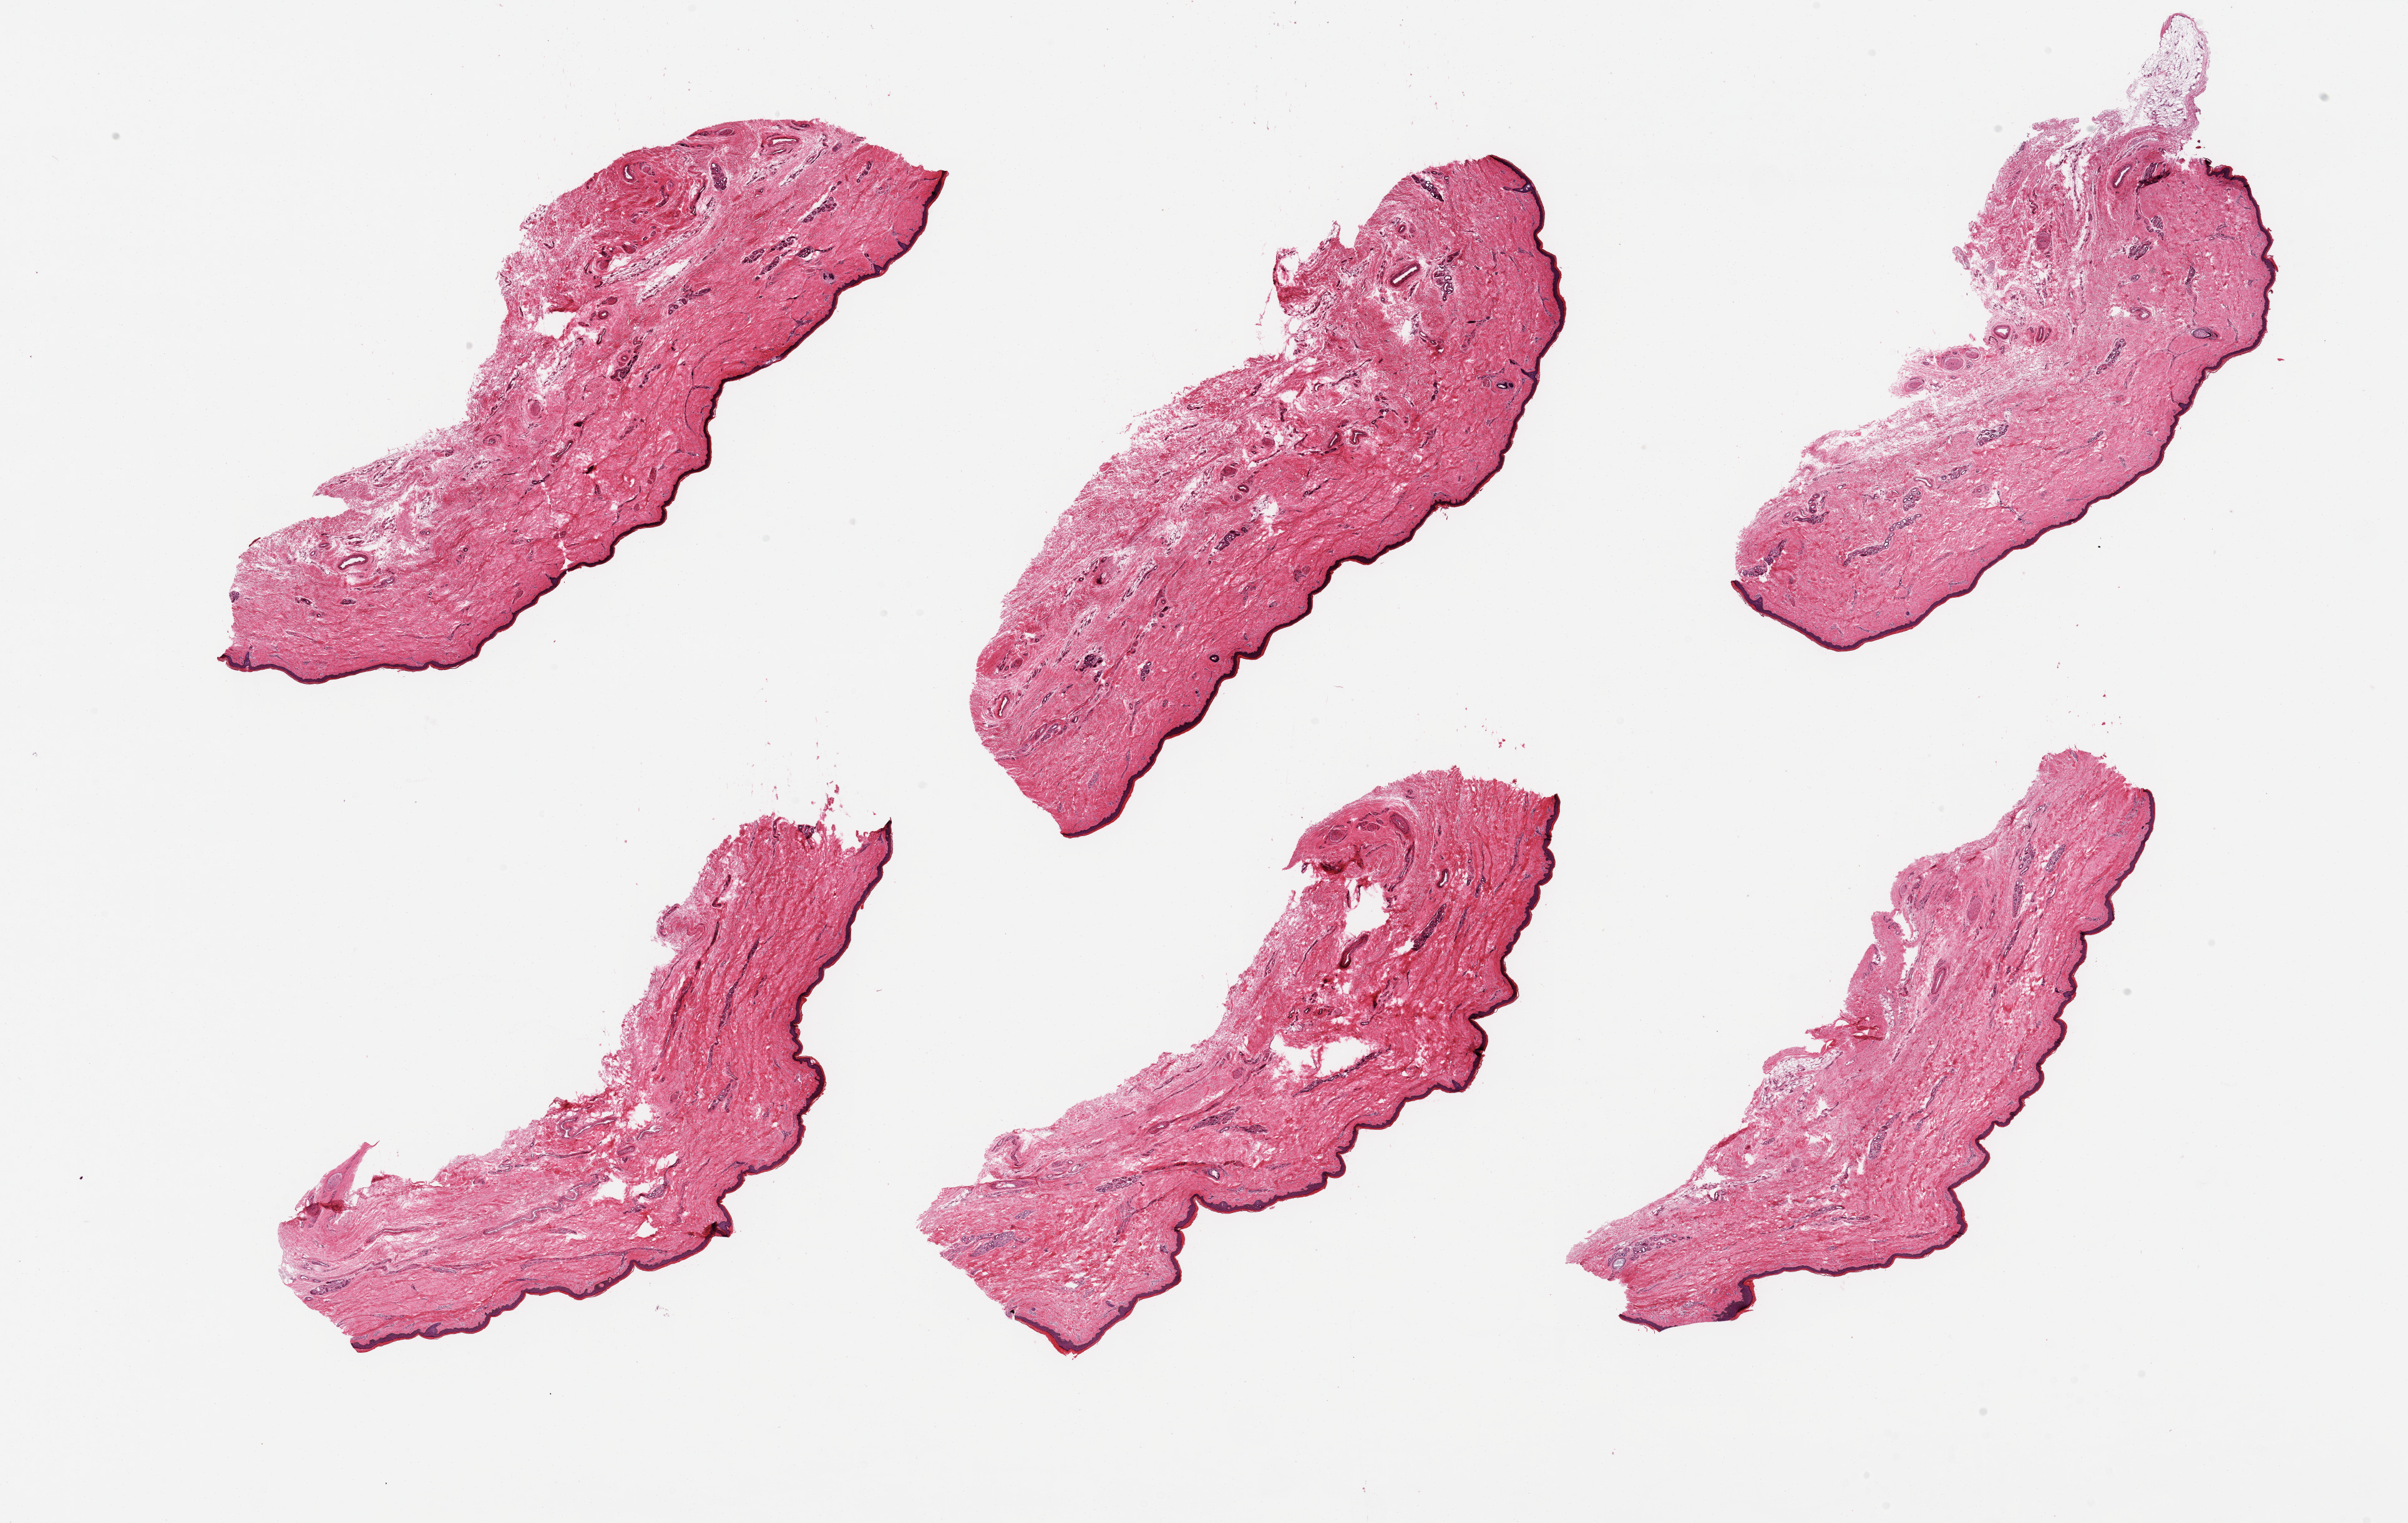
Digitized haematoxylin and eosin-stained section, brightfield — low-resolution overview of the scanned area, about 30.5 x 19.3 mm, PAXgene-fixed paraffin-embedded (PFPE) section, section of skin of lower leg (target tissue), tissue donor sample.
Reviewer comment on this tissue sample: 6 pieces, no dermal fat; squamous epithelium is ~40-45 microns.